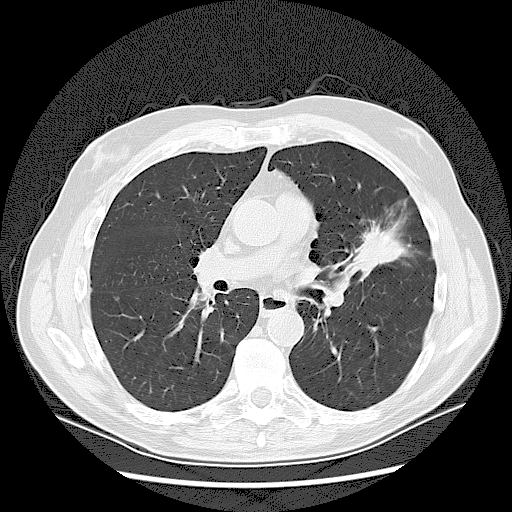
Low-dose screening chest CT, one axial slice. Position 72 of 132 along the scan axis. 120 kVp. Lung window (W 1500 / L -600 HU). 2.5 mm slice thickness. 512 × 512 image matrix.
Outlined on this slice (manually delineated by an expert):
- lesion 1 (tumor, upper lobe of left lung): bounding box <359,225,405,266> (left, top, right, bottom; pixels)